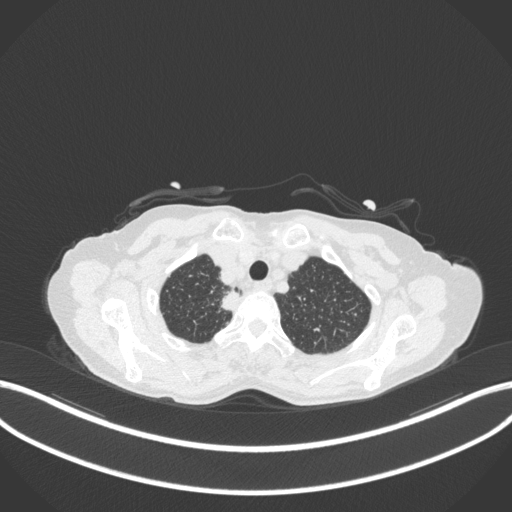
Chest CT, one axial slice; slice 329 of 363 in the series (ordered by position); reconstruction kernel B31f; lung window (W 1500 / L -600 HU); 512 × 512 image matrix, field of view 400 × 400 mm. Female patient, age 75 years. Case-level facts recorded for this patient, not image findings: clinical TNM (as recorded): T1c N1 M1.
Outlined on this slice (rectangle marked by the reading radiologist):
- lung tumour (recorded histology: adenocarcinoma): bounding box [x1, y1, x2, y2] px = [215, 289, 248, 318]